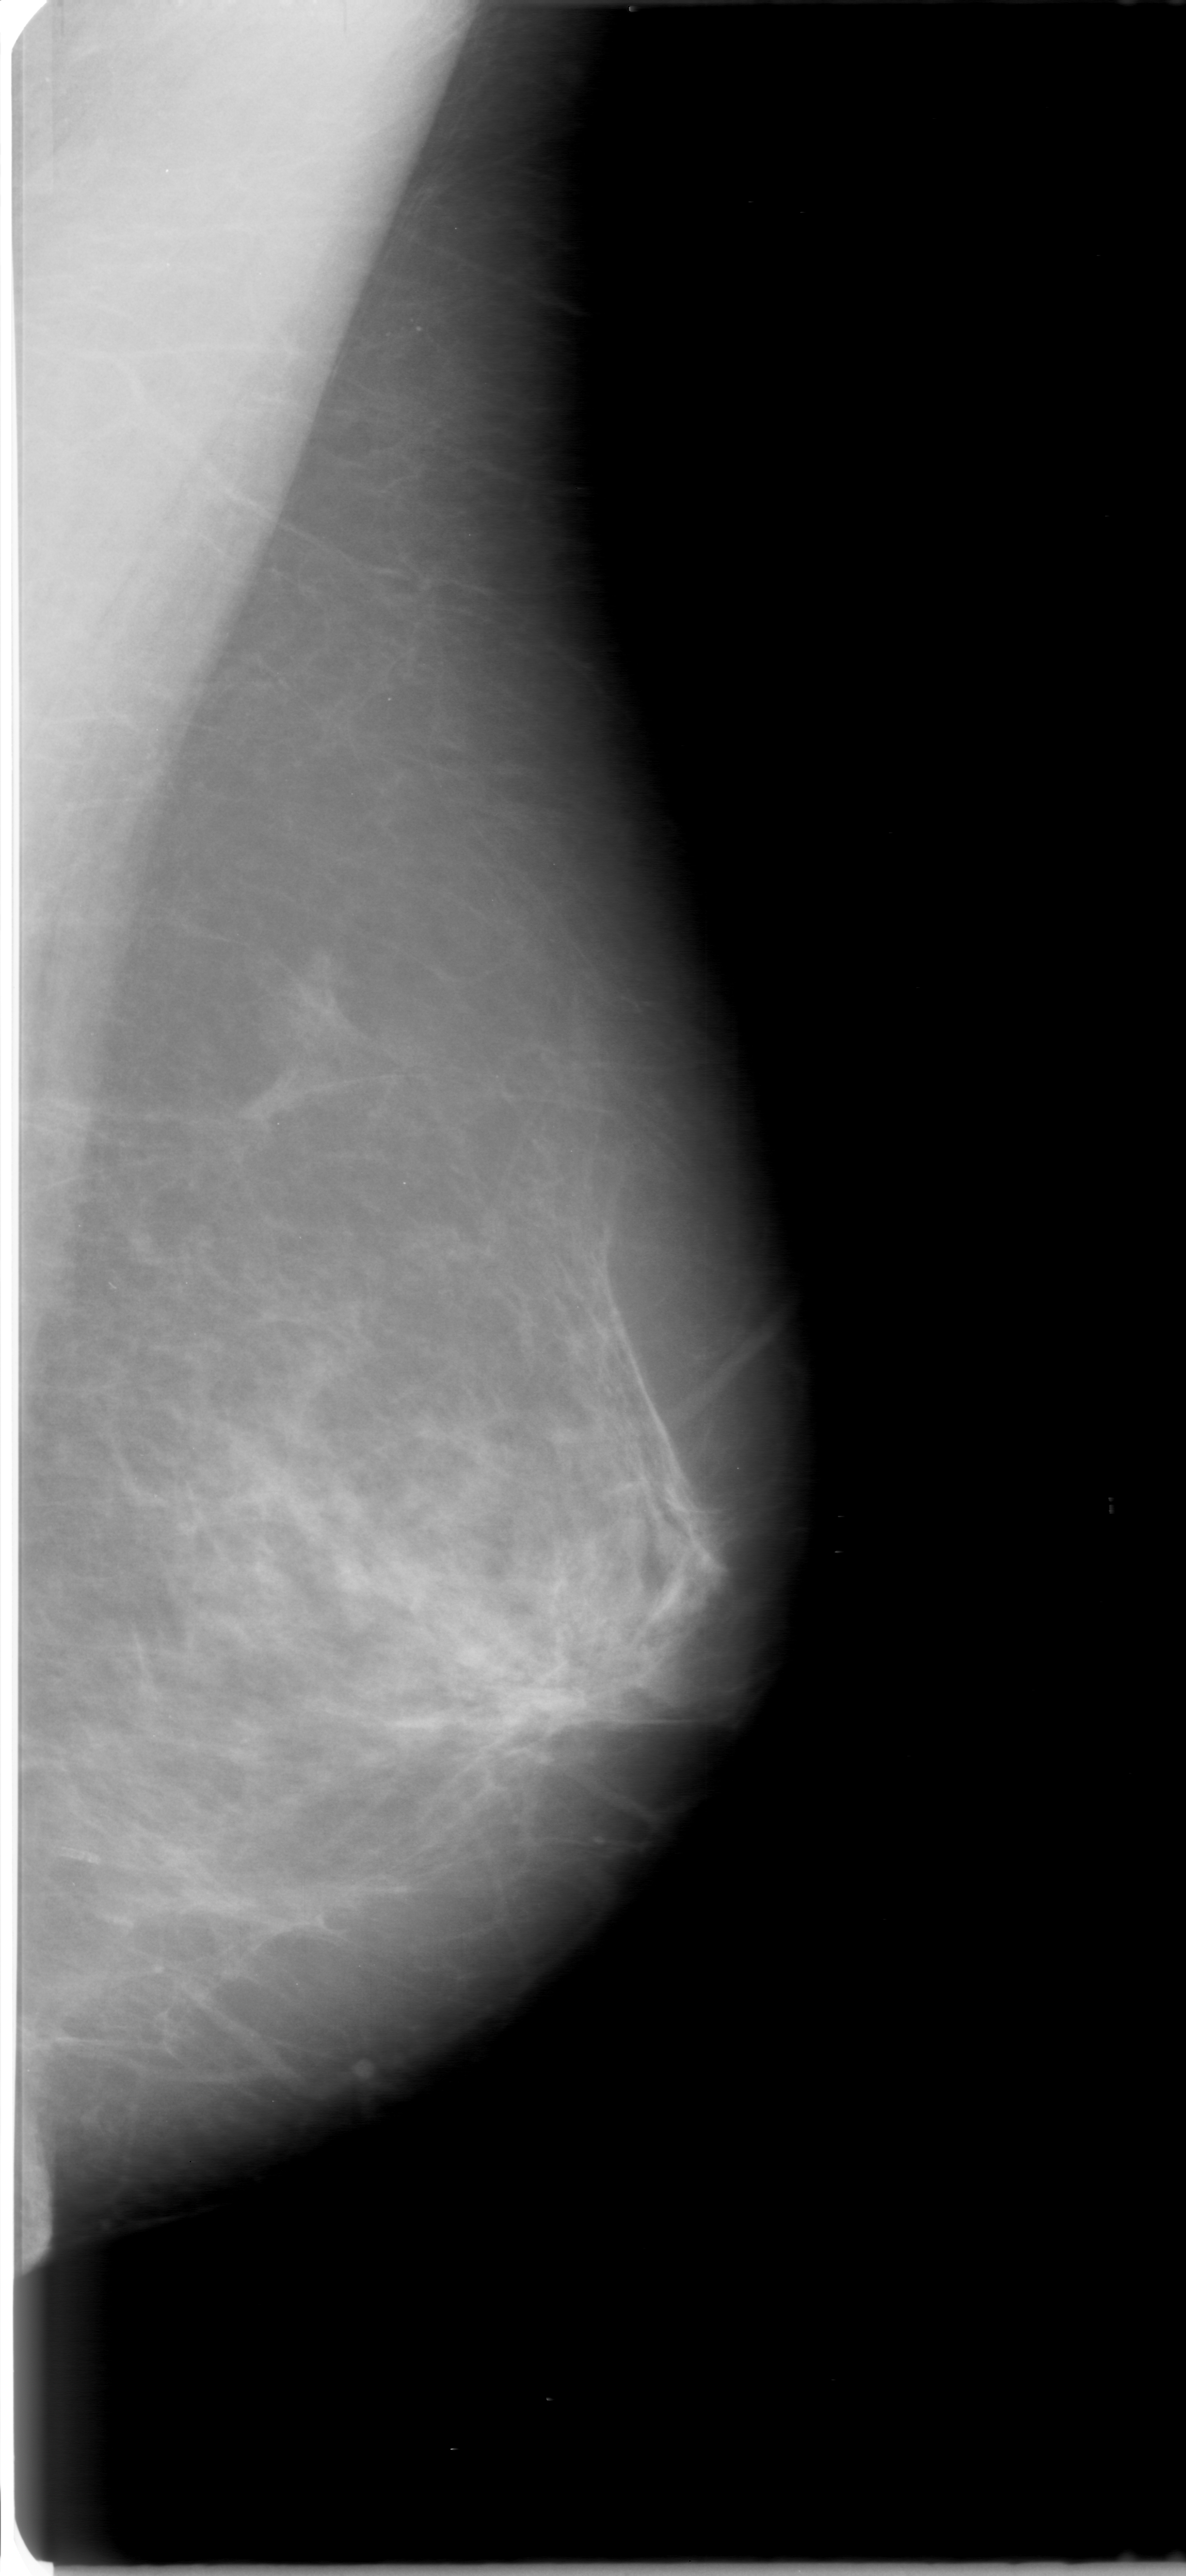
Mammogram (digitized film), left breast, mediolateral oblique (MLO) view, BI-RADS breast density category 2 (scale 1–4).
Abnormality record for this image: mass, shape irregular, margins ill defined; BI-RADS assessment category 2; pathology (as recorded): benign.